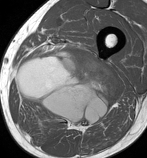
MRI of an extremity soft-tissue mass, one axial slice. Slice 55 of 86 in the series (ordered by position). MR volume resampled by the dataset authors to the PET/CT grid (not the native acquisition matrix). 3.27 mm slice thickness. 147 × 158 image matrix, field of view 144 × 154 mm. Male patient. Case-level facts recorded for this patient, not image findings: histological type: undifferentiated pleomorphic liposarcoma; grade: high; site of the primary tumour: left thigh.
Outlined on this slice (expert contour drawn on MRI and transferred to this co-registered scan by the dataset authors):
- gross tumour volume including surrounding oedema: box from (x=16, y=47) to (x=118, y=130) px
- gross tumour volume (mass): (x=16, y=47)–(x=118, y=127)